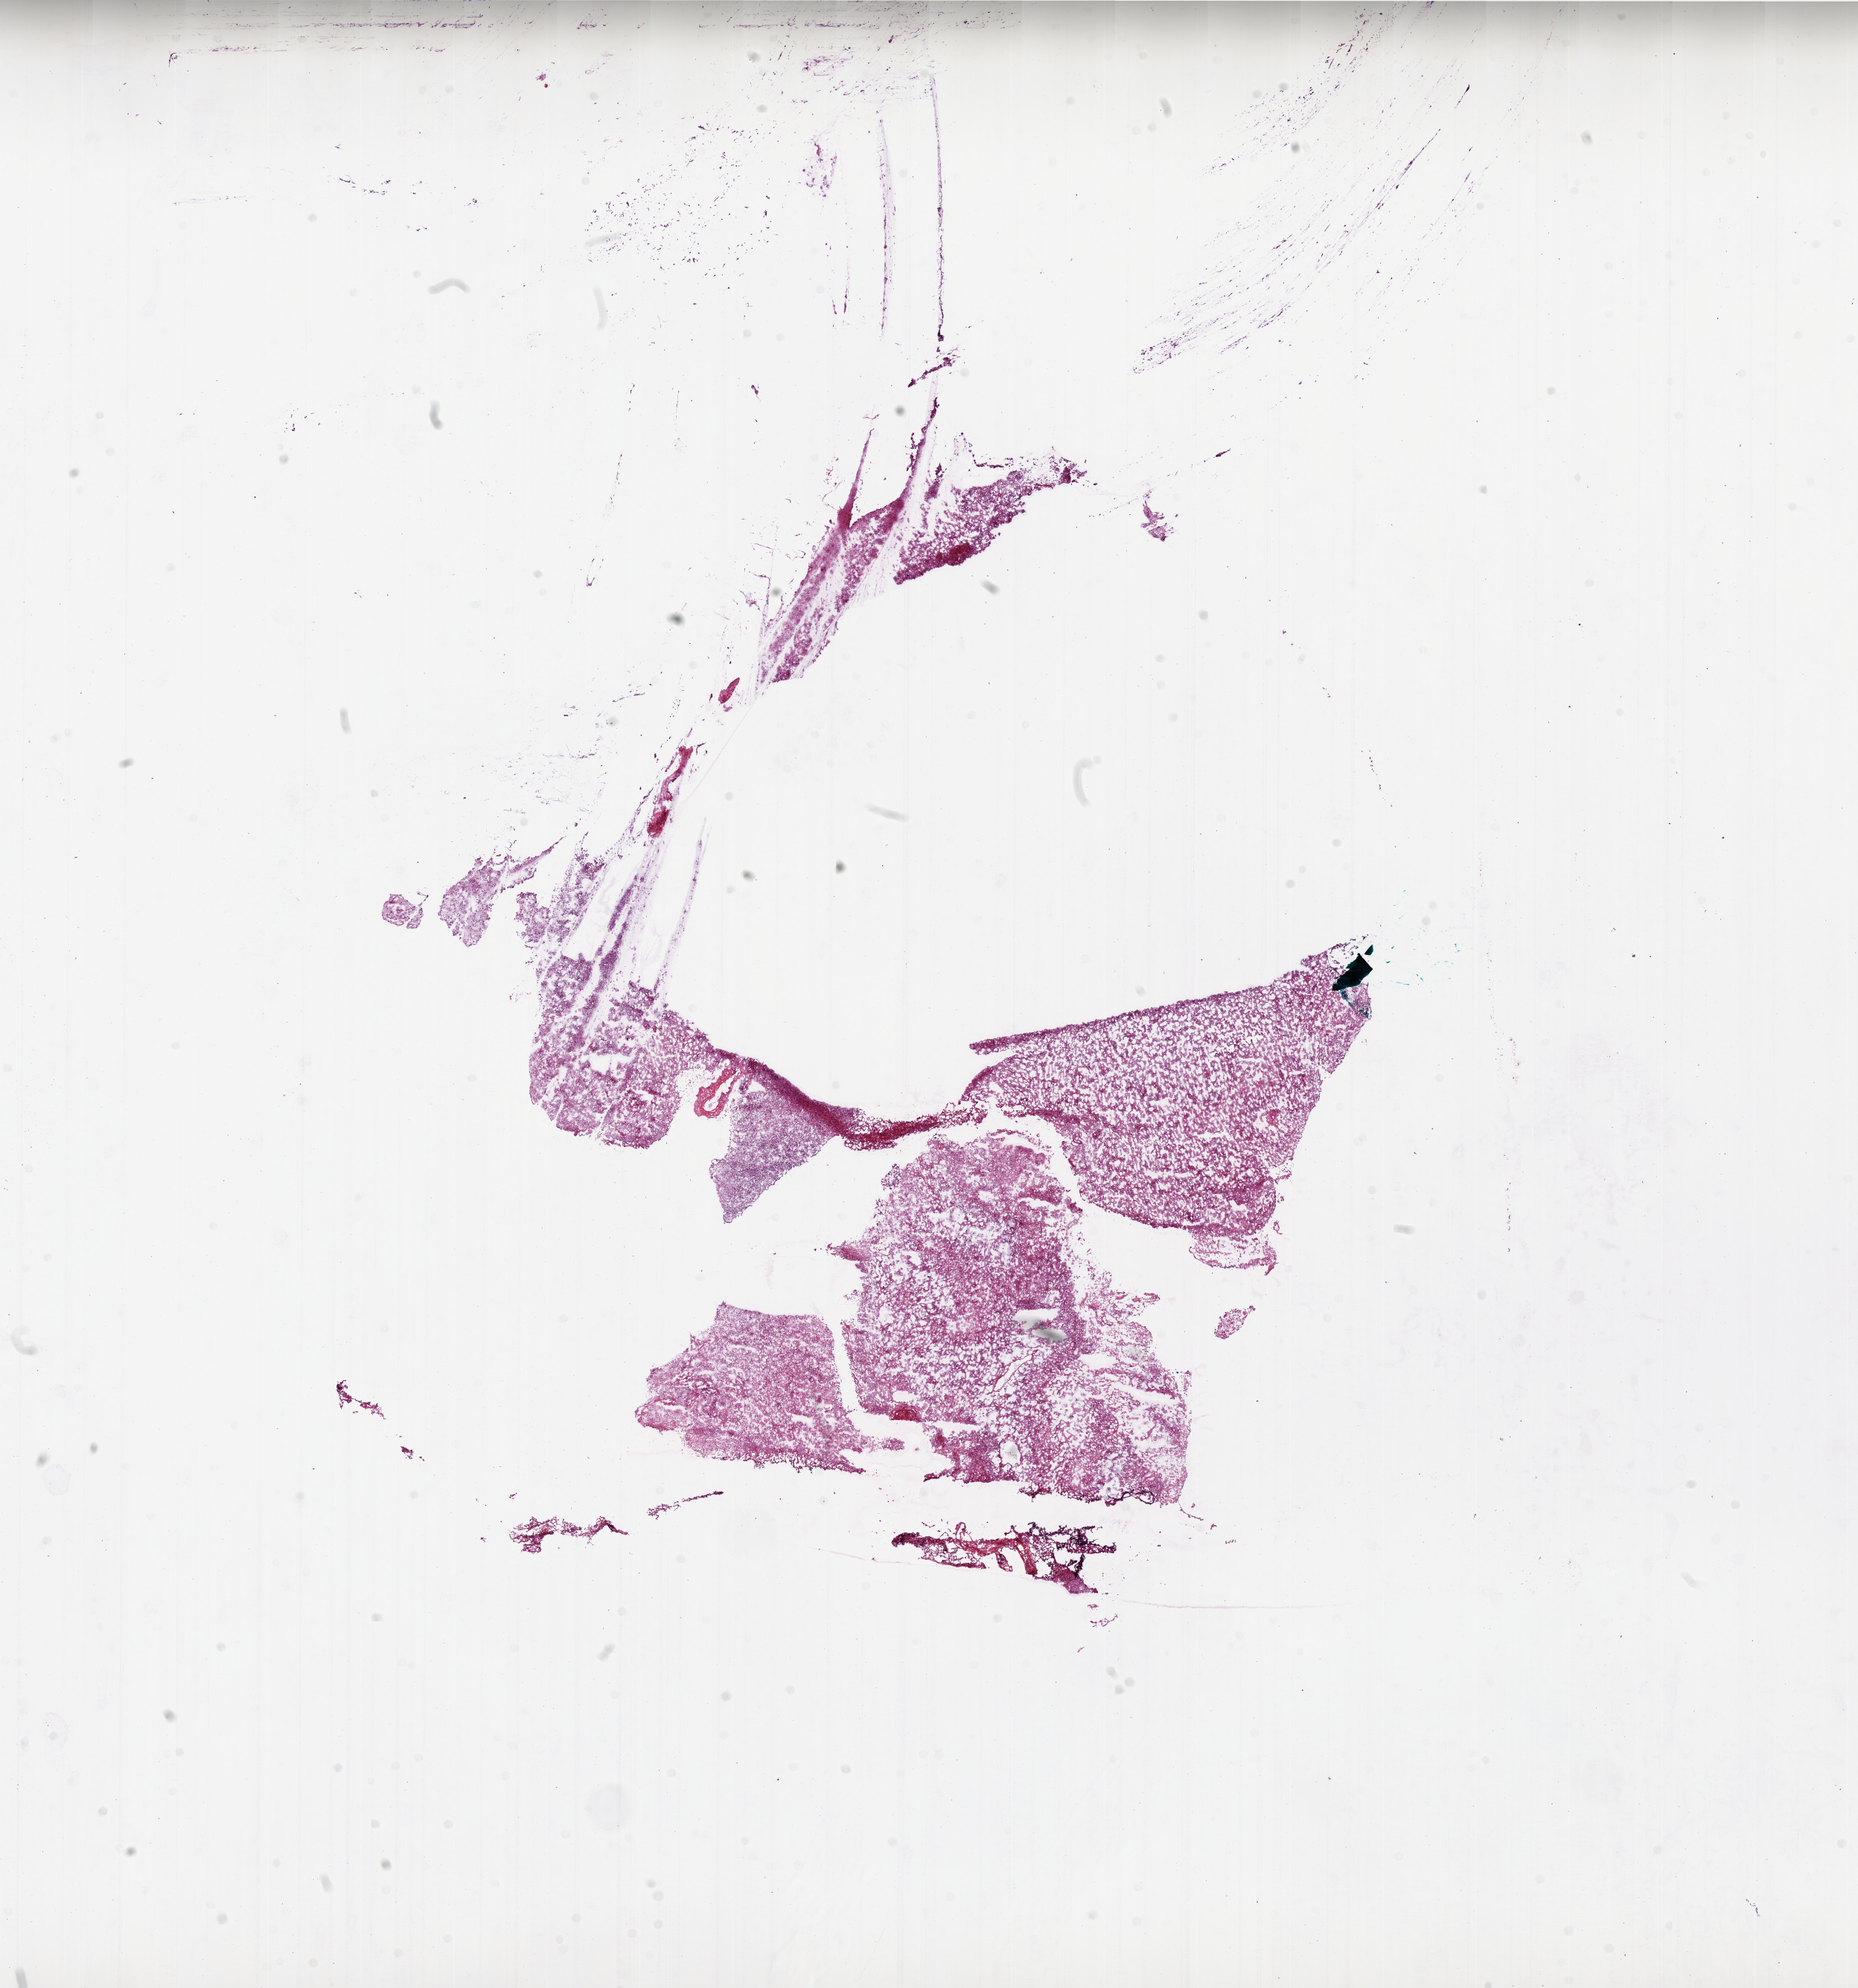
H&E whole-slide image — shown as a low-resolution overview of the whole scanned area (about 20.0 x 21.4 mm, from a 20x scan). Composition of this section per pathologist review: tumour cells 50%, tumour nuclei 100%, normal cells 0%, stromal cells 0%, necrosis 50%.
Specimen: frozen section from the bottom of the tissue portion; brain, primary tumour sample.